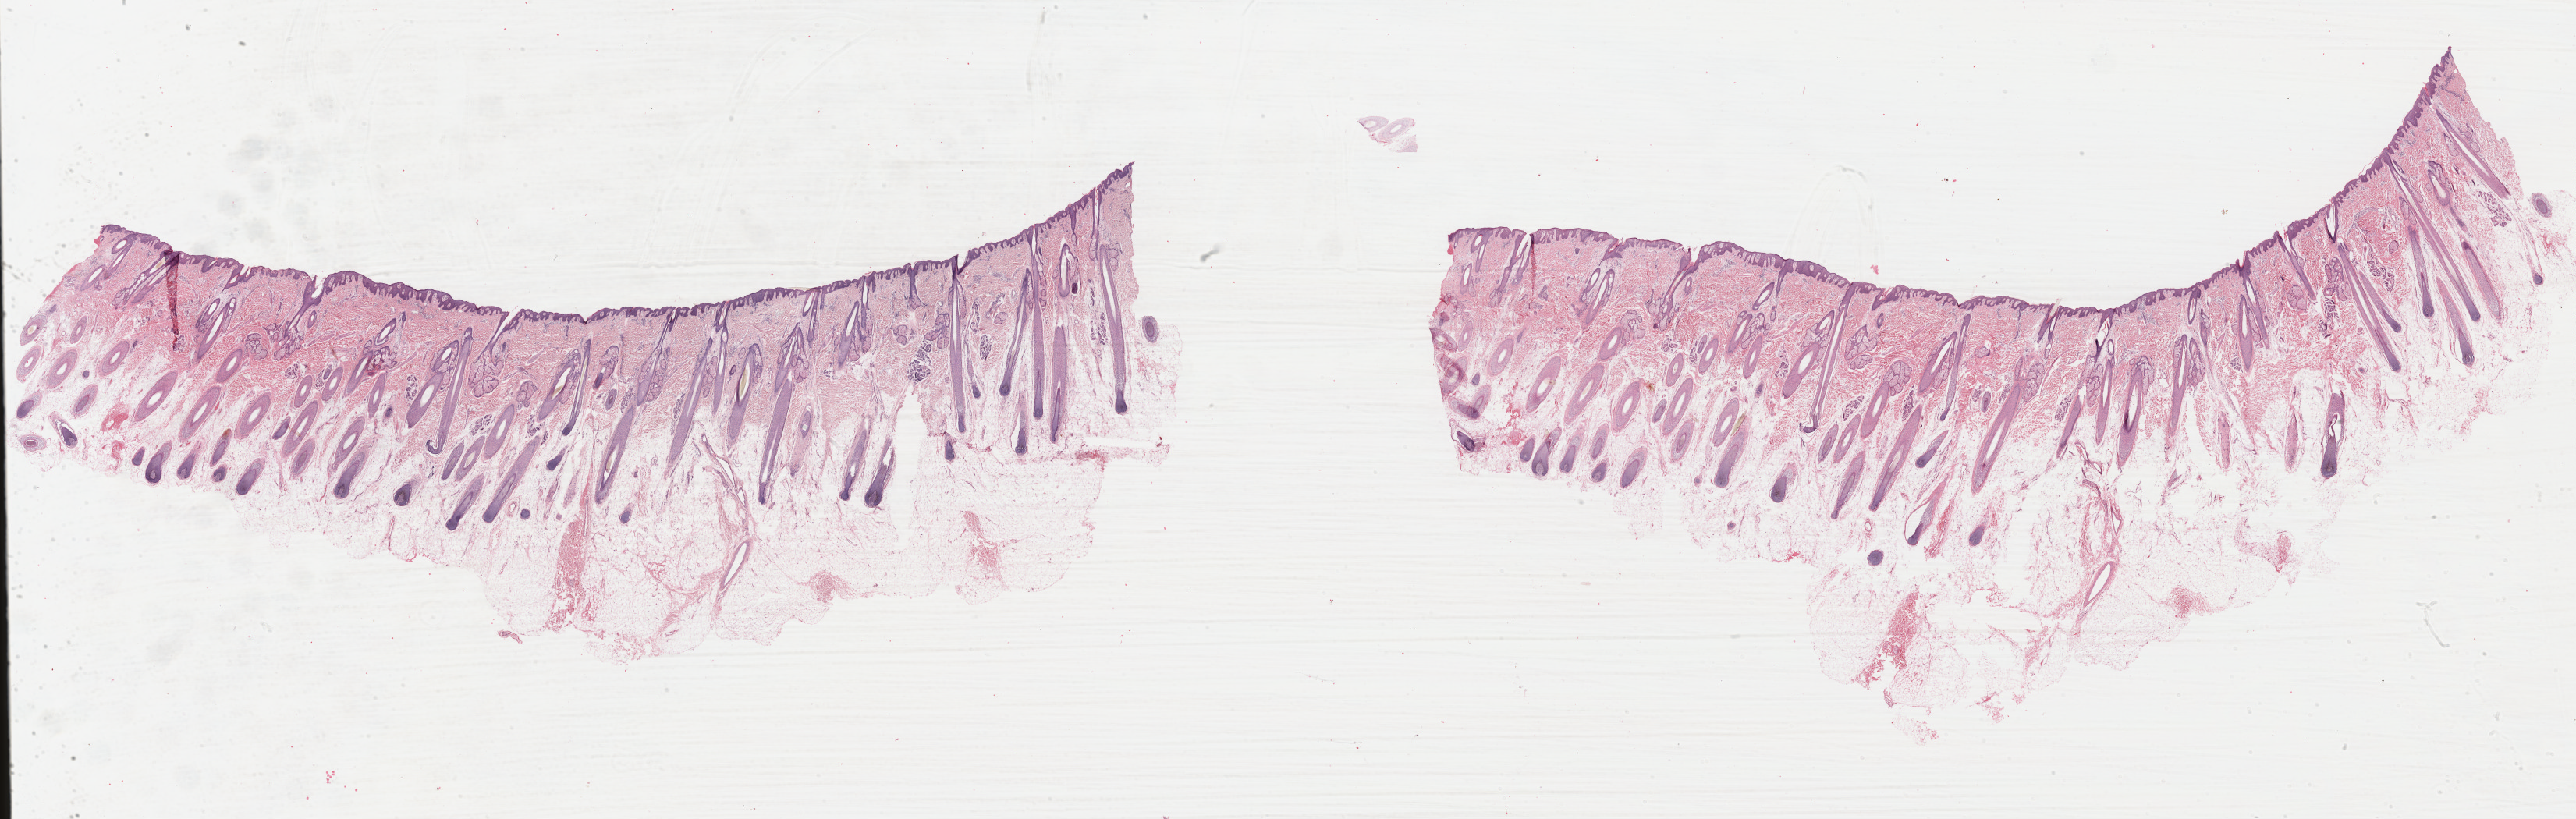
Whole-slide histology image, Hematoxylin and eosin (H&E) stained — whole scanned area (about 51.9 x 16.5 mm, slide scanned at 40x) shown as a low-resolution overview, formalin-fixed paraffin-embedded (FFPE) diagnostic section, metastatic tumour sample, sampled site not recorded. Male, age 19 years at initial diagnosis.
• this section: metastatic tumour tissue
• patient diagnosis: Malignant melanoma, NOS